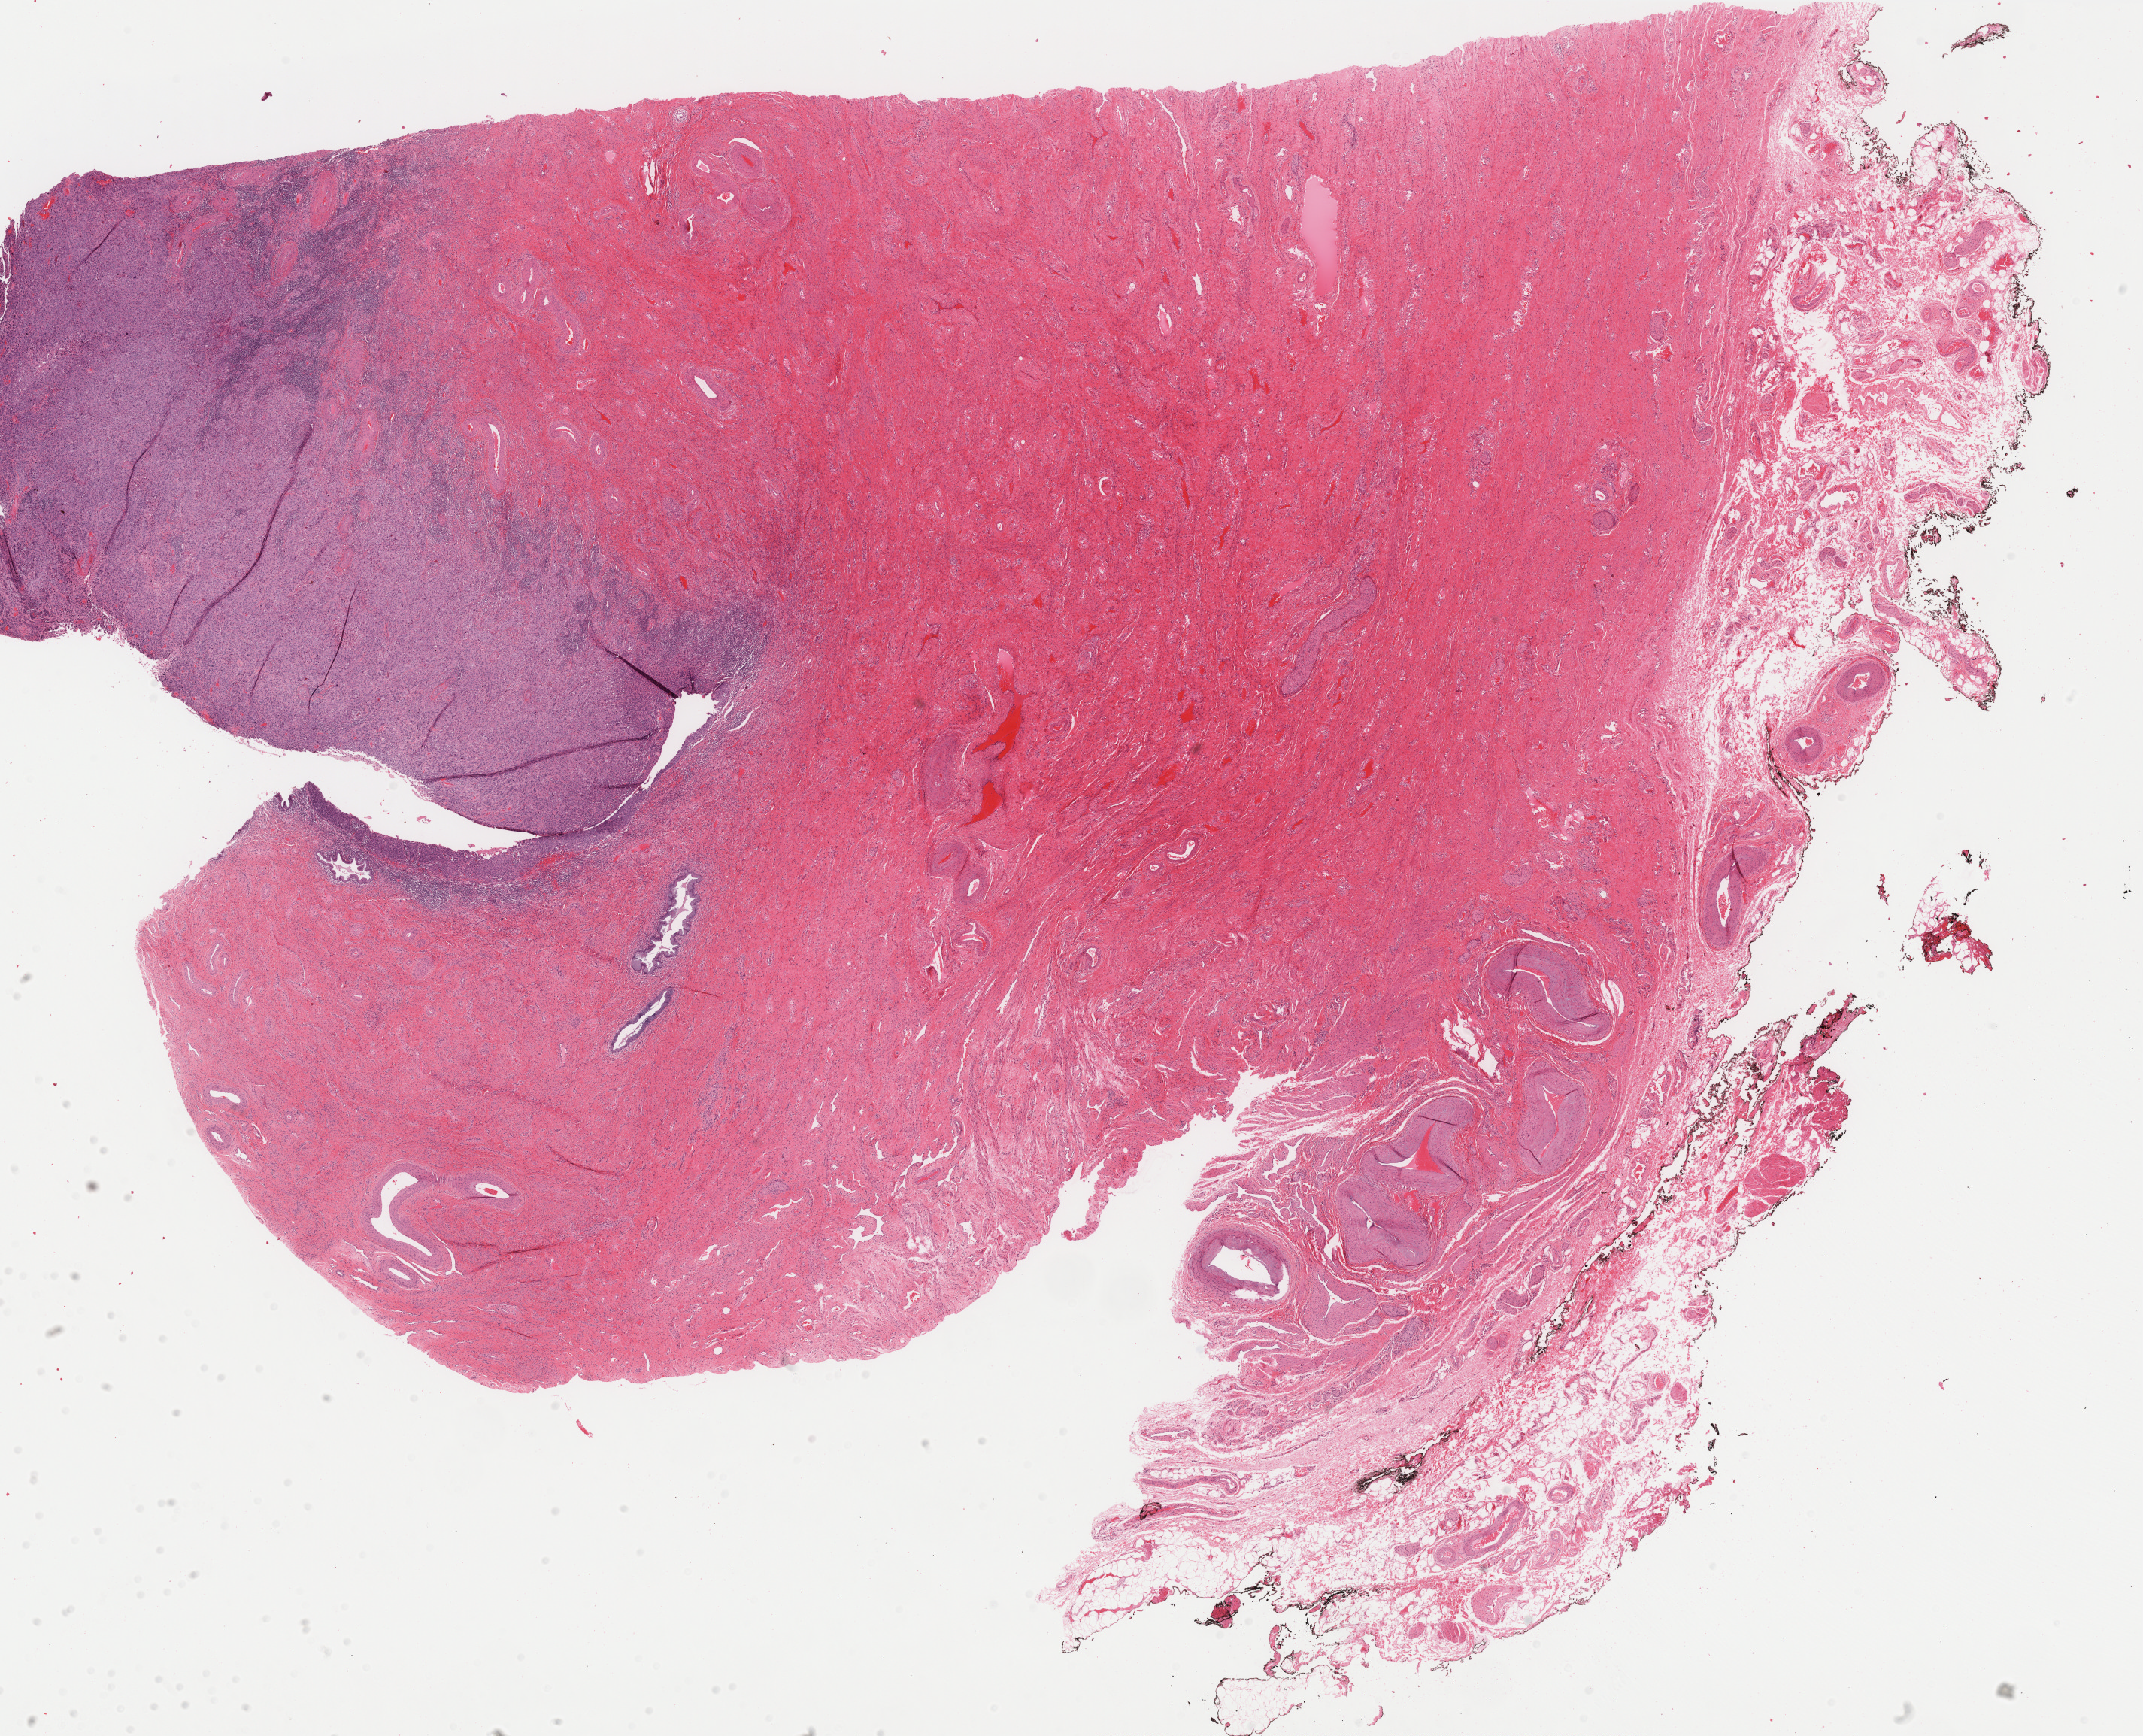
Hematoxylin and eosin (H&E) stained whole-slide image — a low-resolution overview of the entire scanned area, about 22.8 x 18.5 mm. Formalin-fixed paraffin-embedded (FFPE) diagnostic section. Sample: primary tumour, cervix. Female patient; age at initial diagnosis 36 years. Histologic grade: G3 (poorly differentiated).
FIGO stage: IB. Pathologic diagnosis: Squamous cell carcinoma, NOS (cervix uteri).